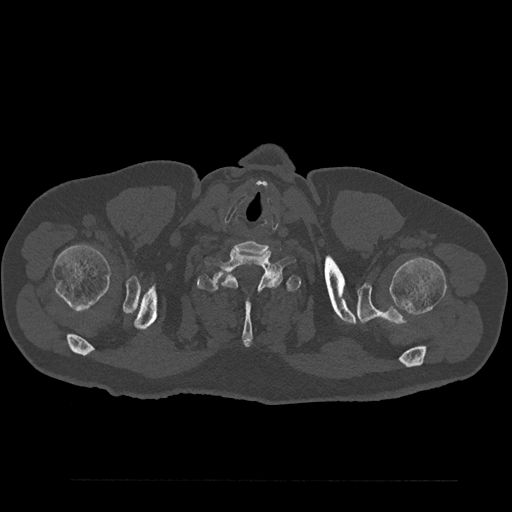
CT including the spine, one axial slice; slice 771 of 797 in the series (ordered by position); reconstruction kernel Br40s/3; bone window (W 1800 / L 400 HU); 0.5 mm slice thickness; 512 × 512 image matrix, field of view 430 × 430 mm. Patient: male, 61 years. From the clinical record (not read from this slice): primary cancer: prostate.
Outlined on this slice (semi-automatic segmentation, software-assisted and operator-edited):
- T1 vertebra: bounding box [x1, y1, x2, y2] px = [197, 257, 301, 346]